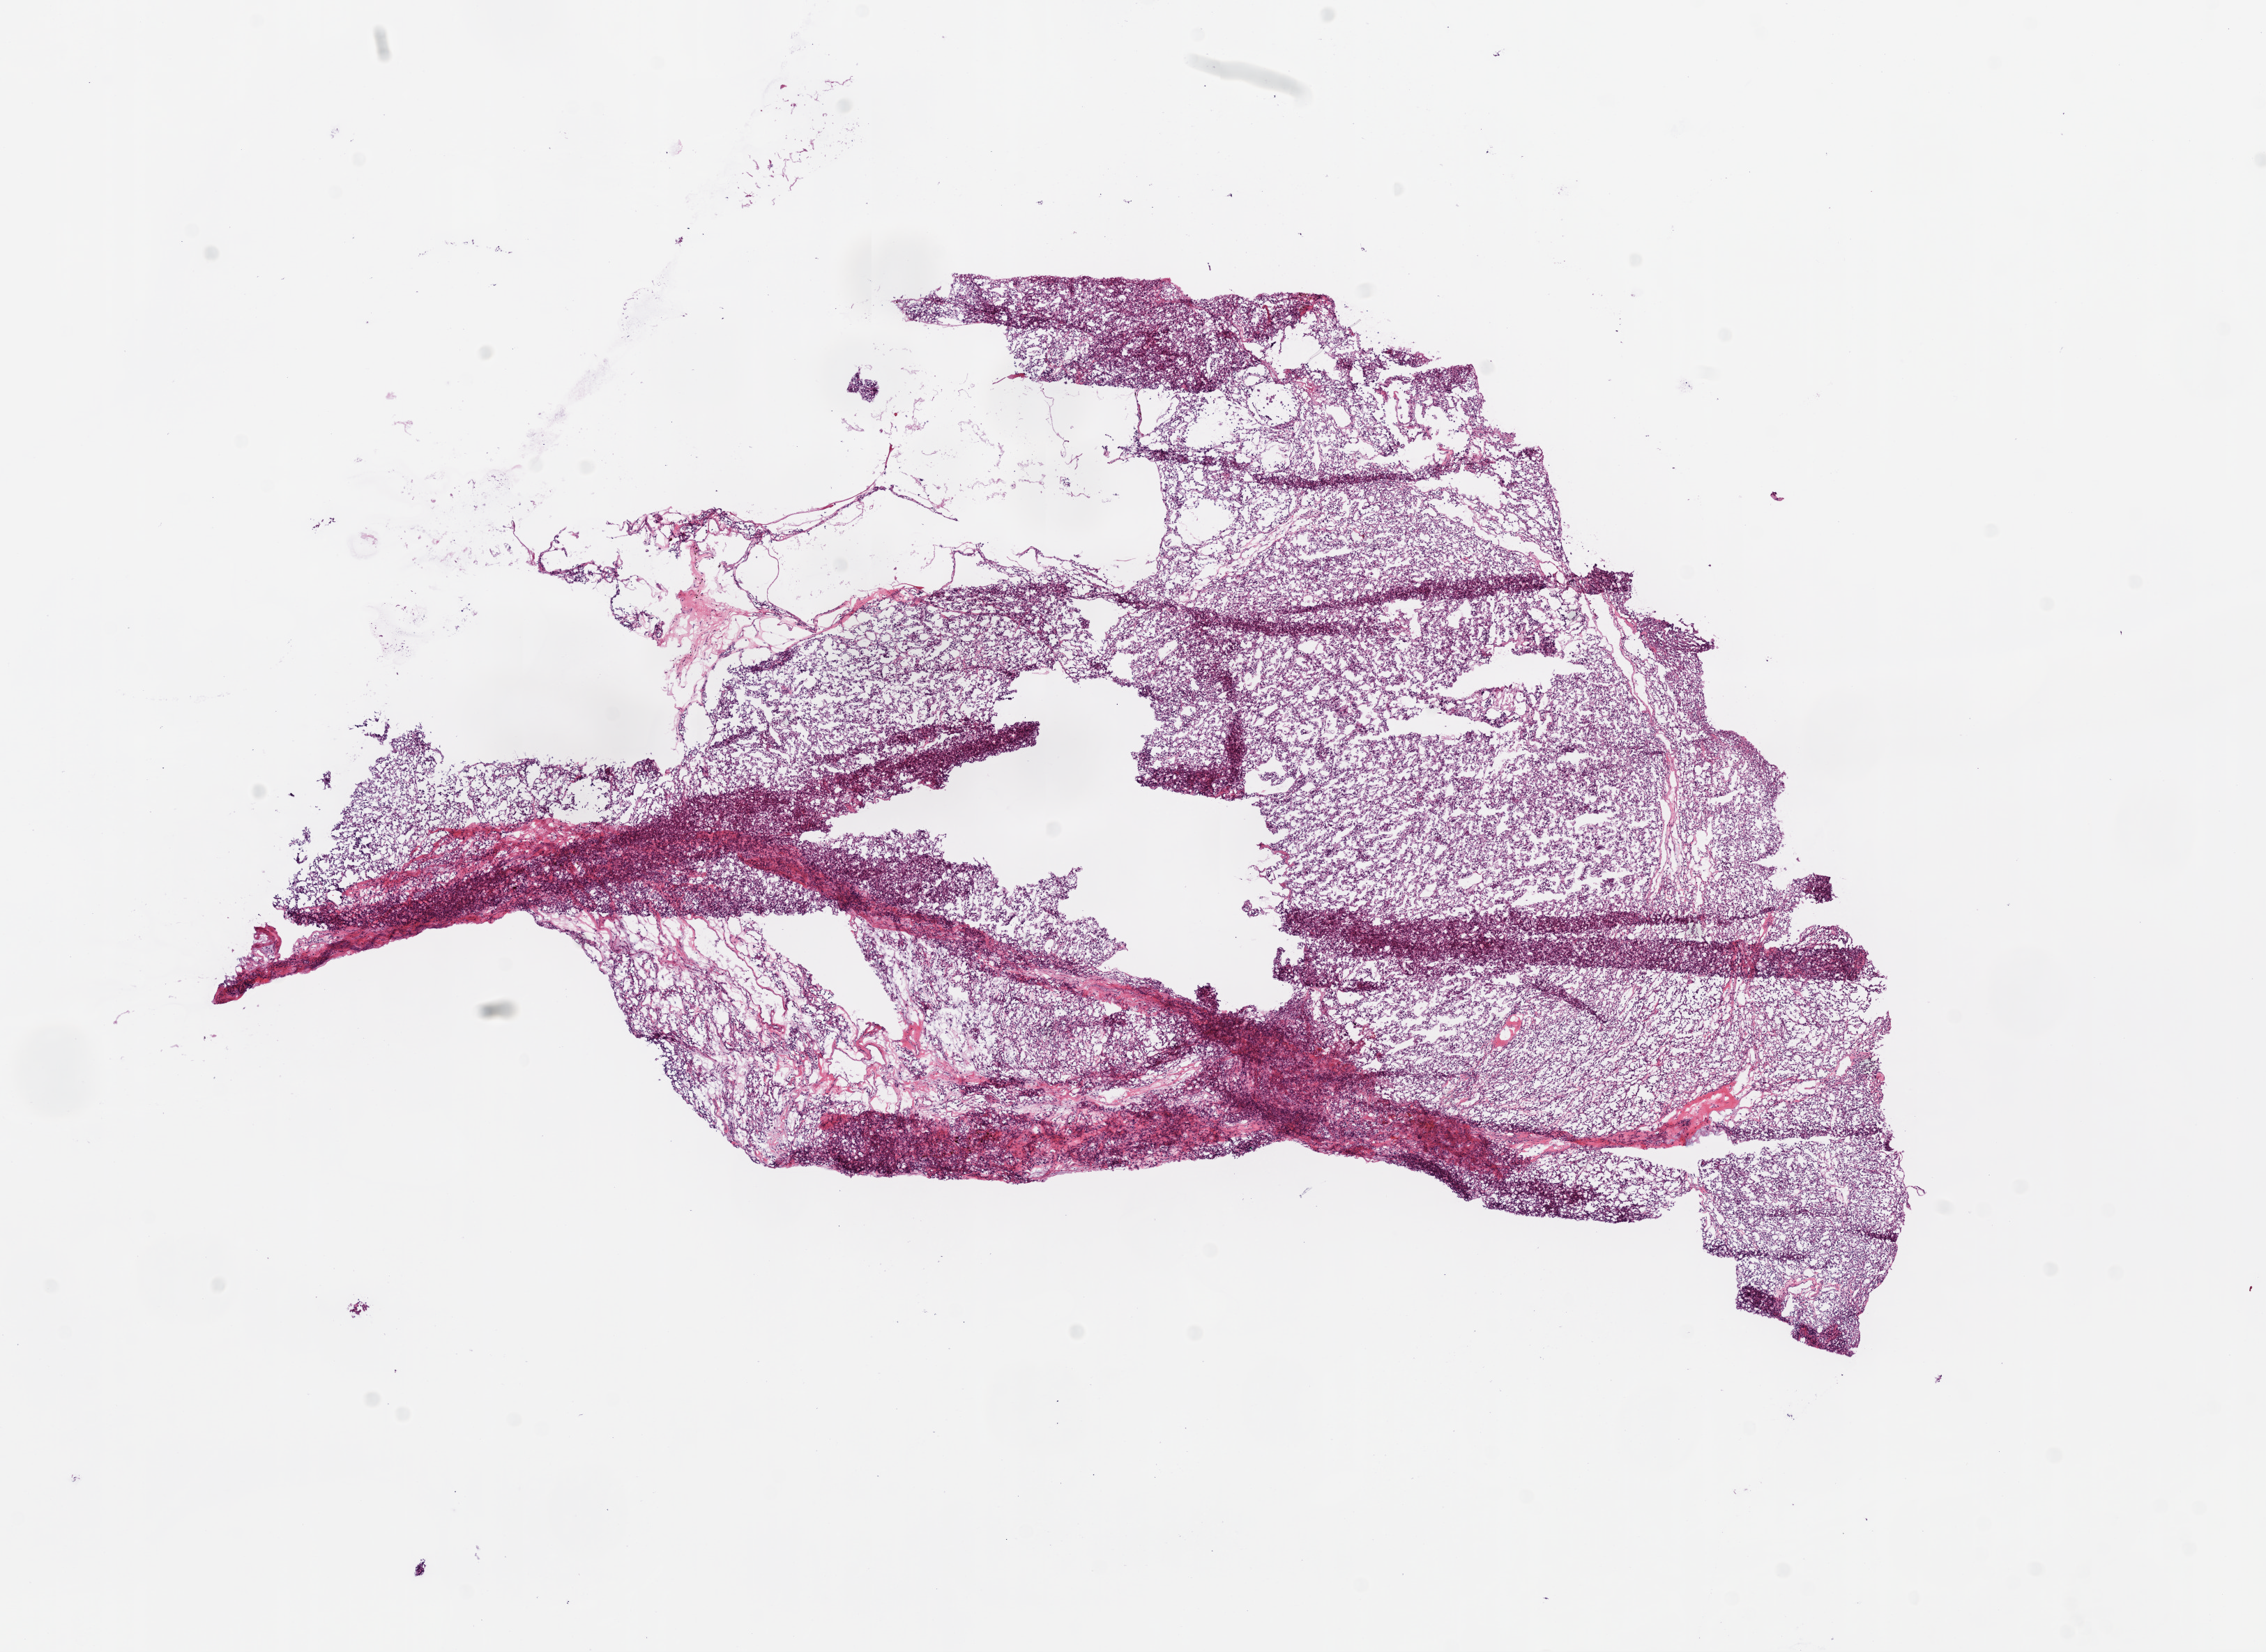
Digitized H&E tissue section (whole slide) — shown as a low-resolution overview of the whole scanned area (about 13.0 x 9.5 mm, acquisition: 20x scan), frozen section, primary tumour sample from the kidney. Male patient; age at initial diagnosis 84 years. Histologic grade: G3 (poorly differentiated). Slide review estimates, as recorded: tumour cells 85%, tumour nuclei 70%, normal cells 0%, stromal cells 15%, necrosis 0%.
Laterality: right. AJCC pathologic stage: I. Pathologic diagnosis: Clear cell adenocarcinoma, NOS.